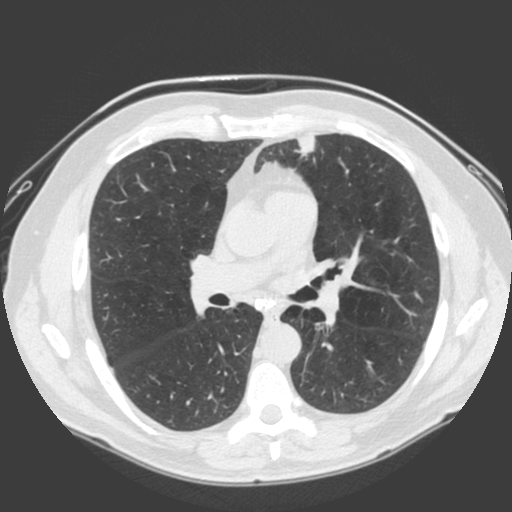
Low-dose screening chest CT, one axial slice. Position 104 of 185 along the scan axis. Lung window (W 1500 / L -600 HU). 2 mm slice thickness. 512 × 512 image matrix.
Structures marked on this image (manually delineated by an expert):
- lesion 1 (tumor, lower lobe of left lung): bounding box [x1, y1, x2, y2] px = [294, 135, 316, 158]